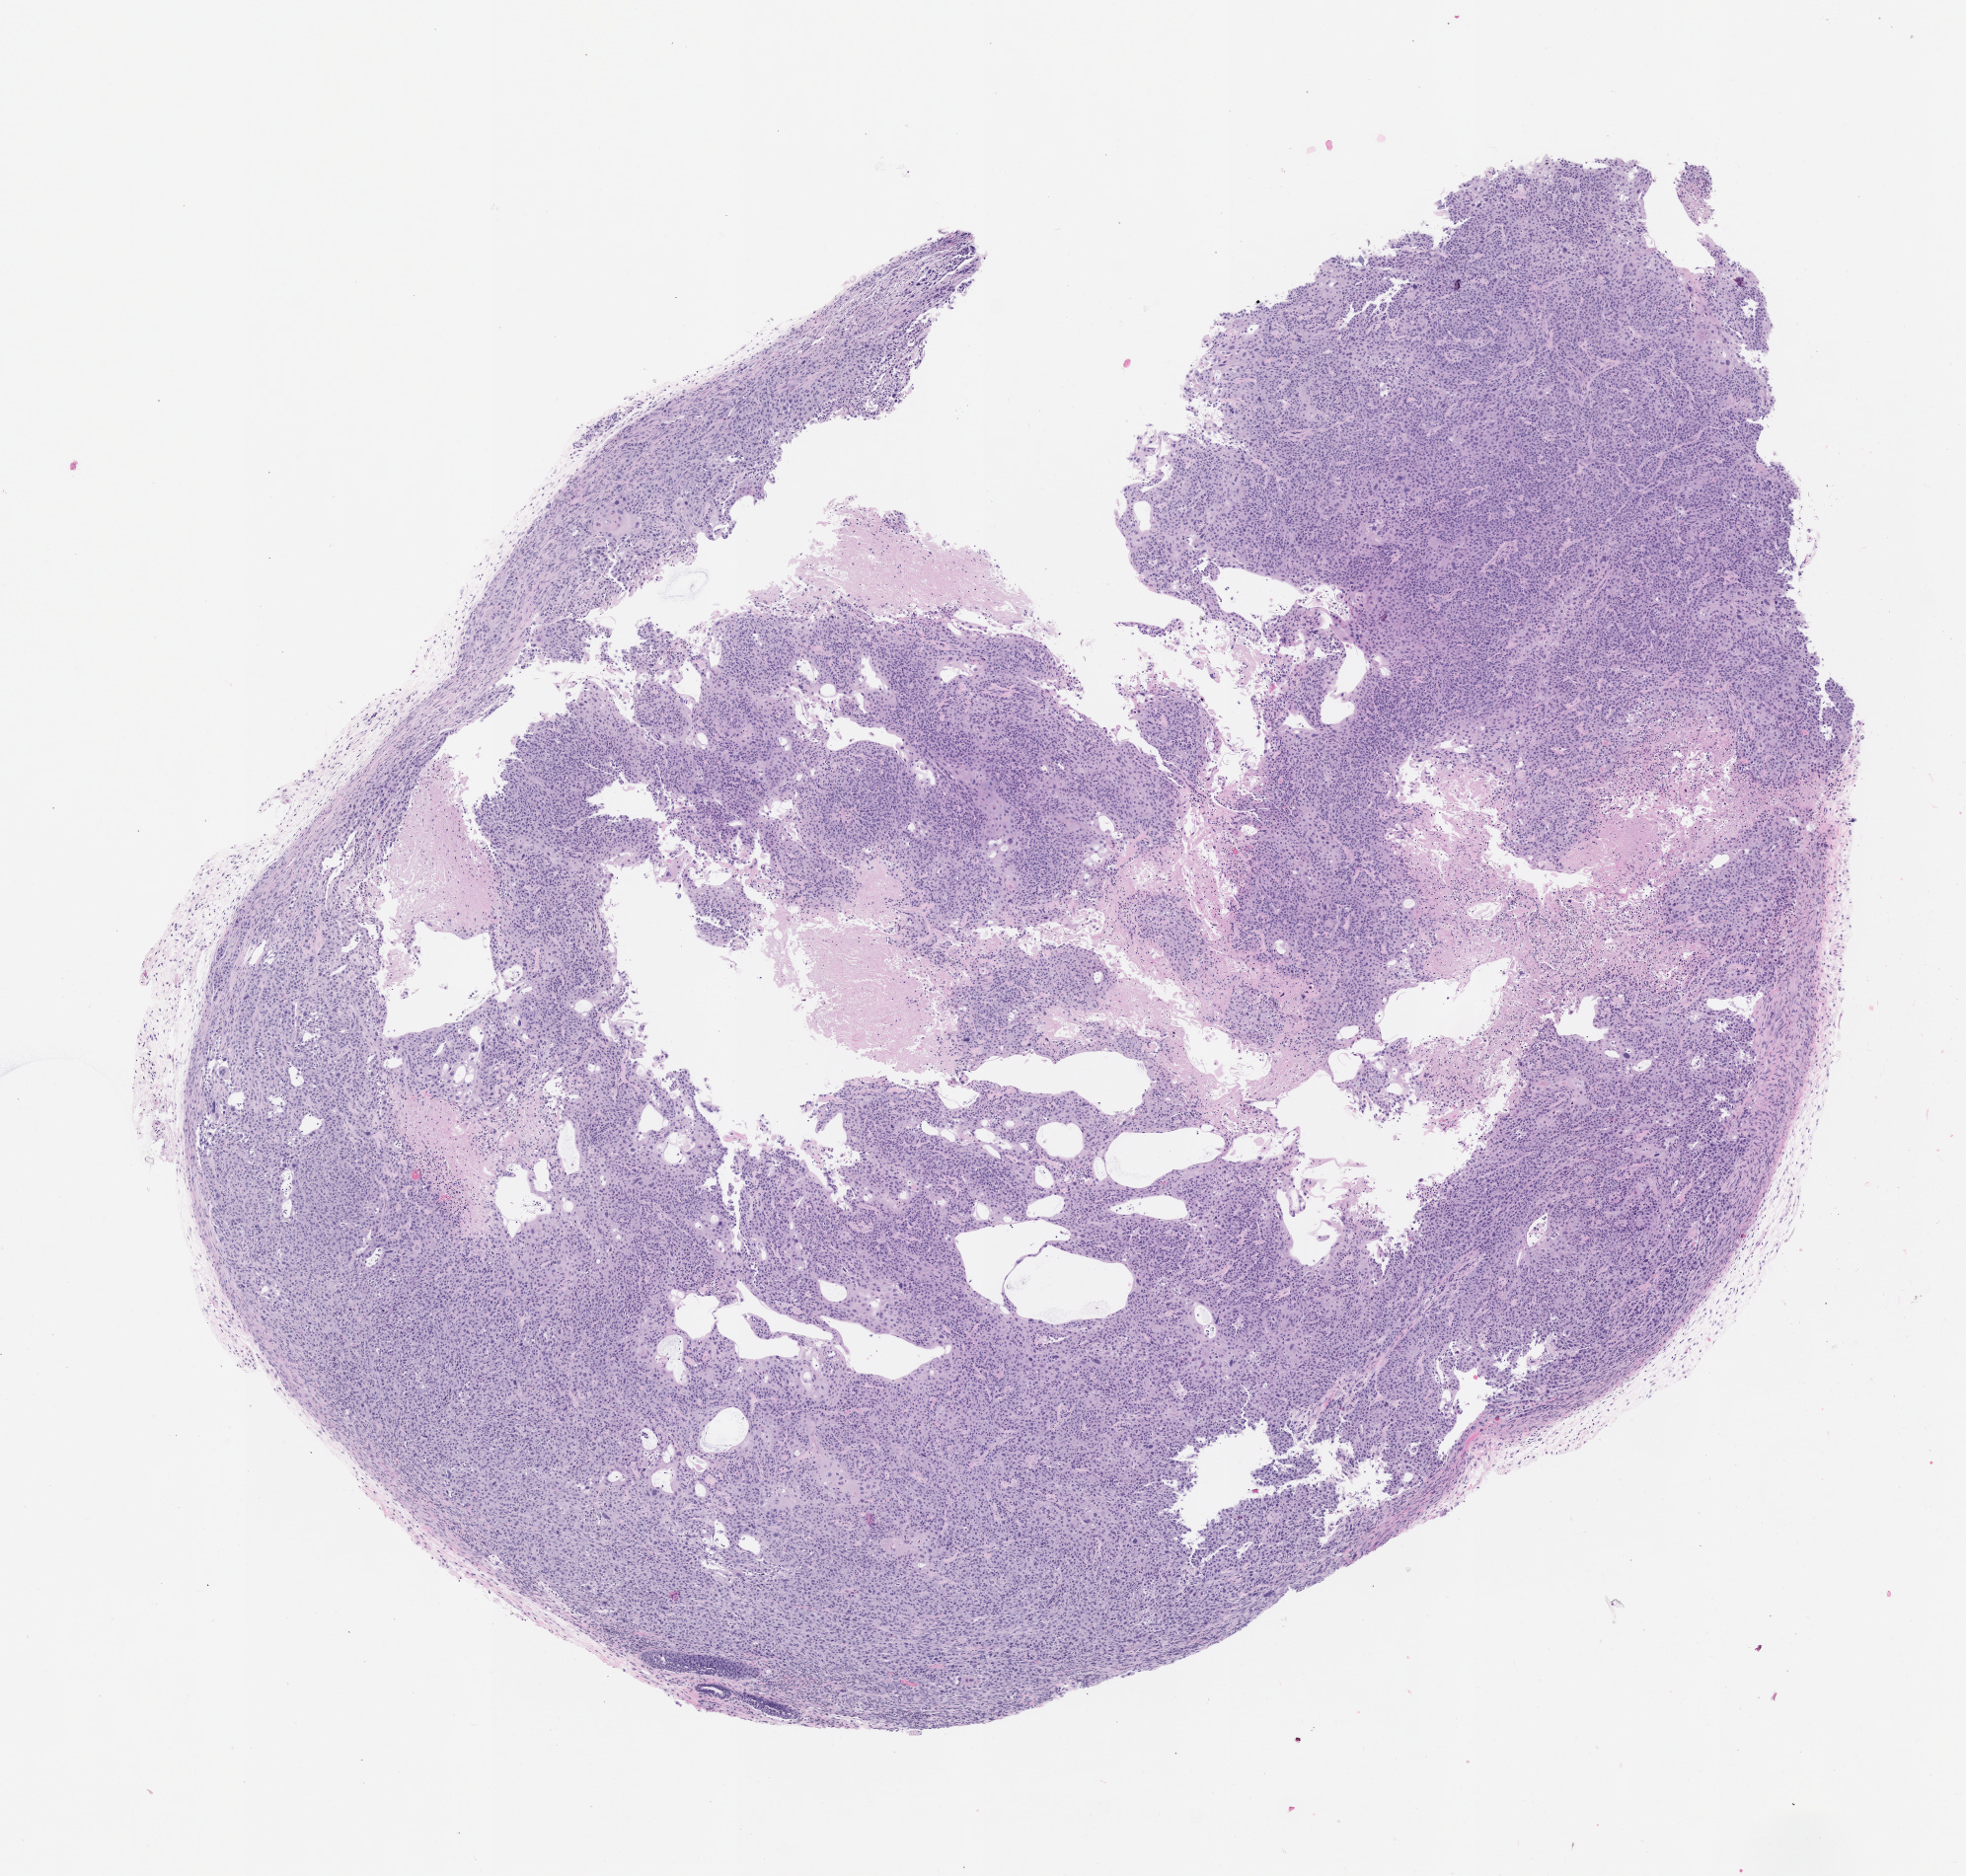
Whole-slide image, H&E: patient-derived xenograft (human tumor grown in a mouse), passage 1, low-resolution overview of the scanned area, about 8.0 x 7.6 mm; FFPE section; tumor site category: head and neck.
Originating patient diagnosis: Mucoepidermoid Carcinoma.